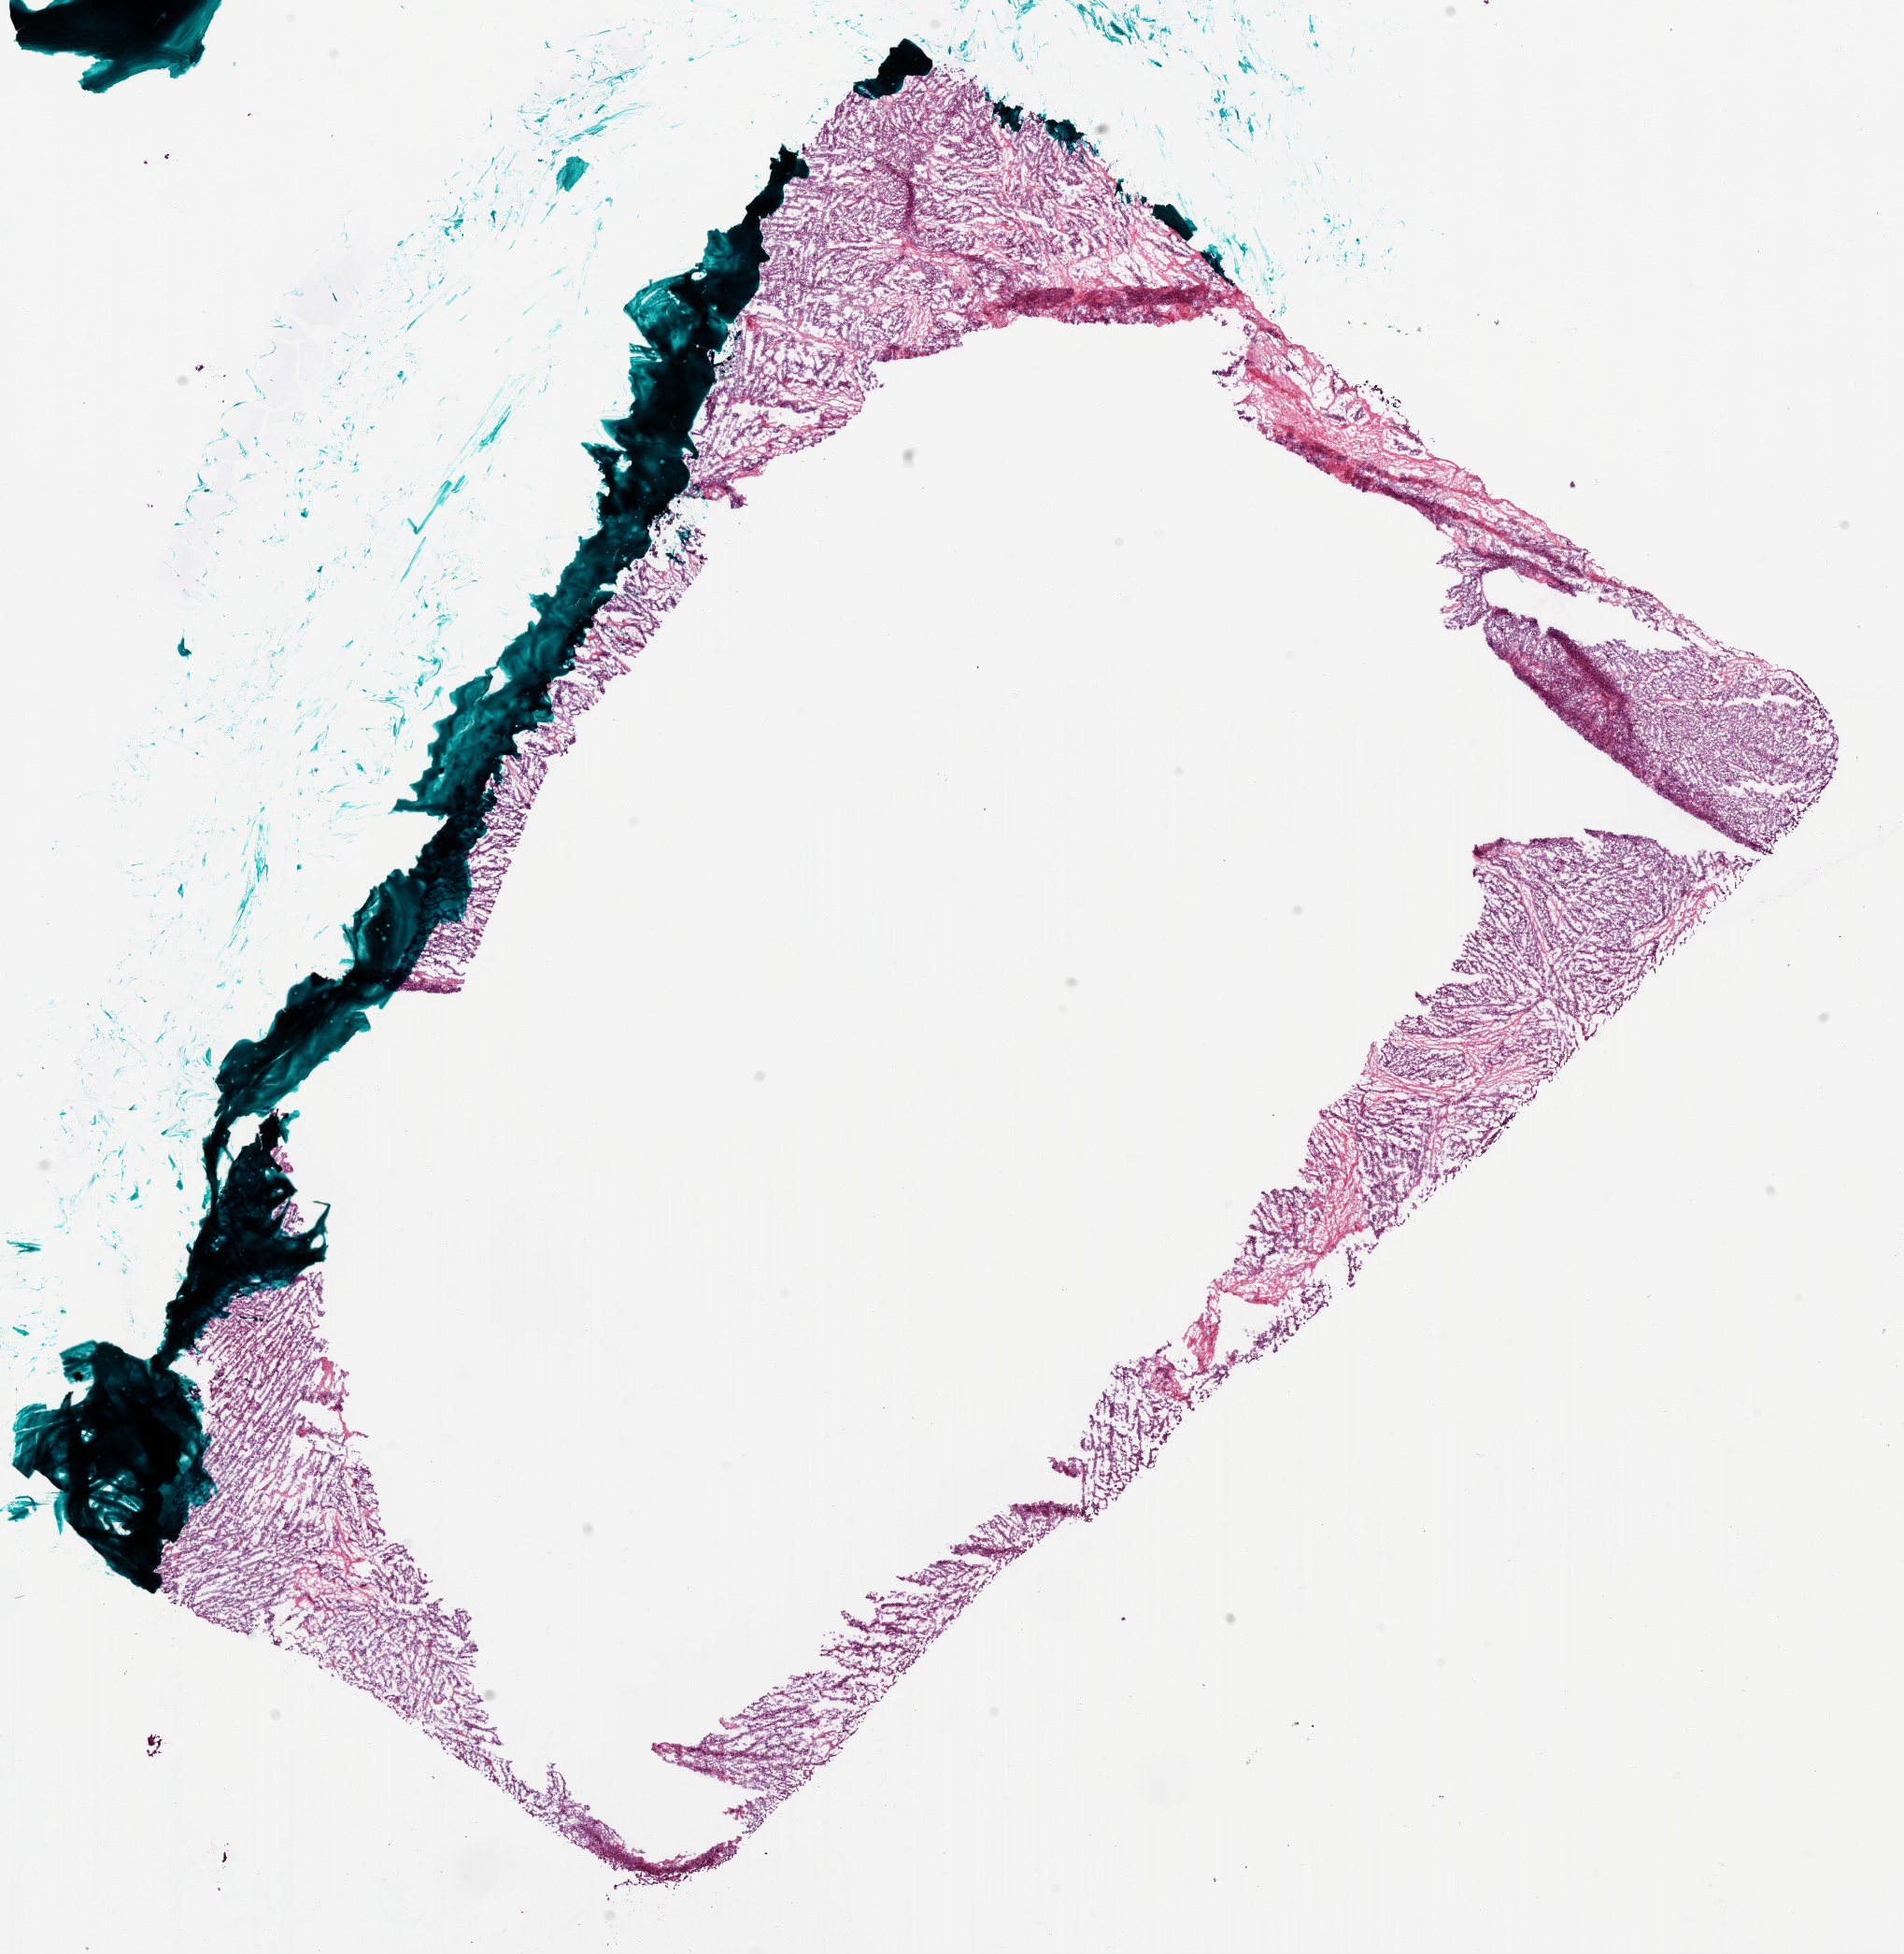
Hematoxylin and eosin (H&E) stained whole-slide image — whole scanned area (about 16.4 x 16.9 mm, from a 20x scan) shown as a low-resolution overview; frozen section from the bottom of the tissue portion; sample: primary tumour, ovary. Patient: female, age at initial diagnosis 63 years. Histologic grade: G3 (poorly differentiated). Composition of this section per pathologist review: tumour cells 89%, tumour nuclei 90%, normal cells 10%, necrosis 1%.
Pathologic diagnosis: Serous cystadenocarcinoma, NOS. FIGO stage: IV.